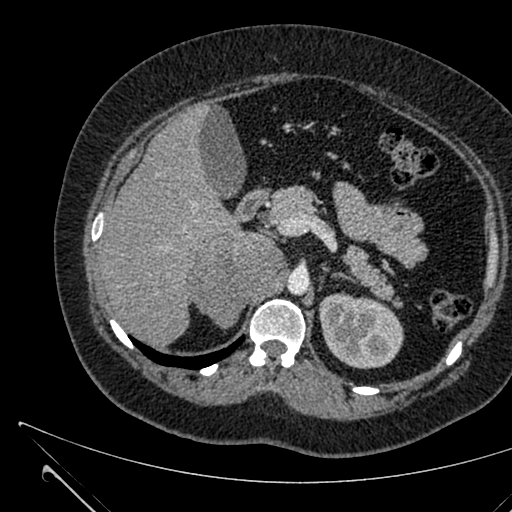
Contrast-enhanced abdominal CT, one axial slice. Slice 421 of 731 in the series (ordered by position). Soft-tissue window (W 400 / L 40 HU). 512 × 512 image matrix, field of view 376 × 376 mm. Female patient, age 36 years. Case-level facts recorded for this patient, not image findings: diagnosis: adrenocortical carcinoma; tumour side: right adrenal; tumour size at pathology: 10 cm; Ki-67 index: 20 %; stage (as recorded): 4.
Structures marked on this image (semi-automatic segmentation, software-assisted and operator-edited):
- mass: bounding box (x1, y1, x2, y2) in pixels: (194, 235, 284, 326)